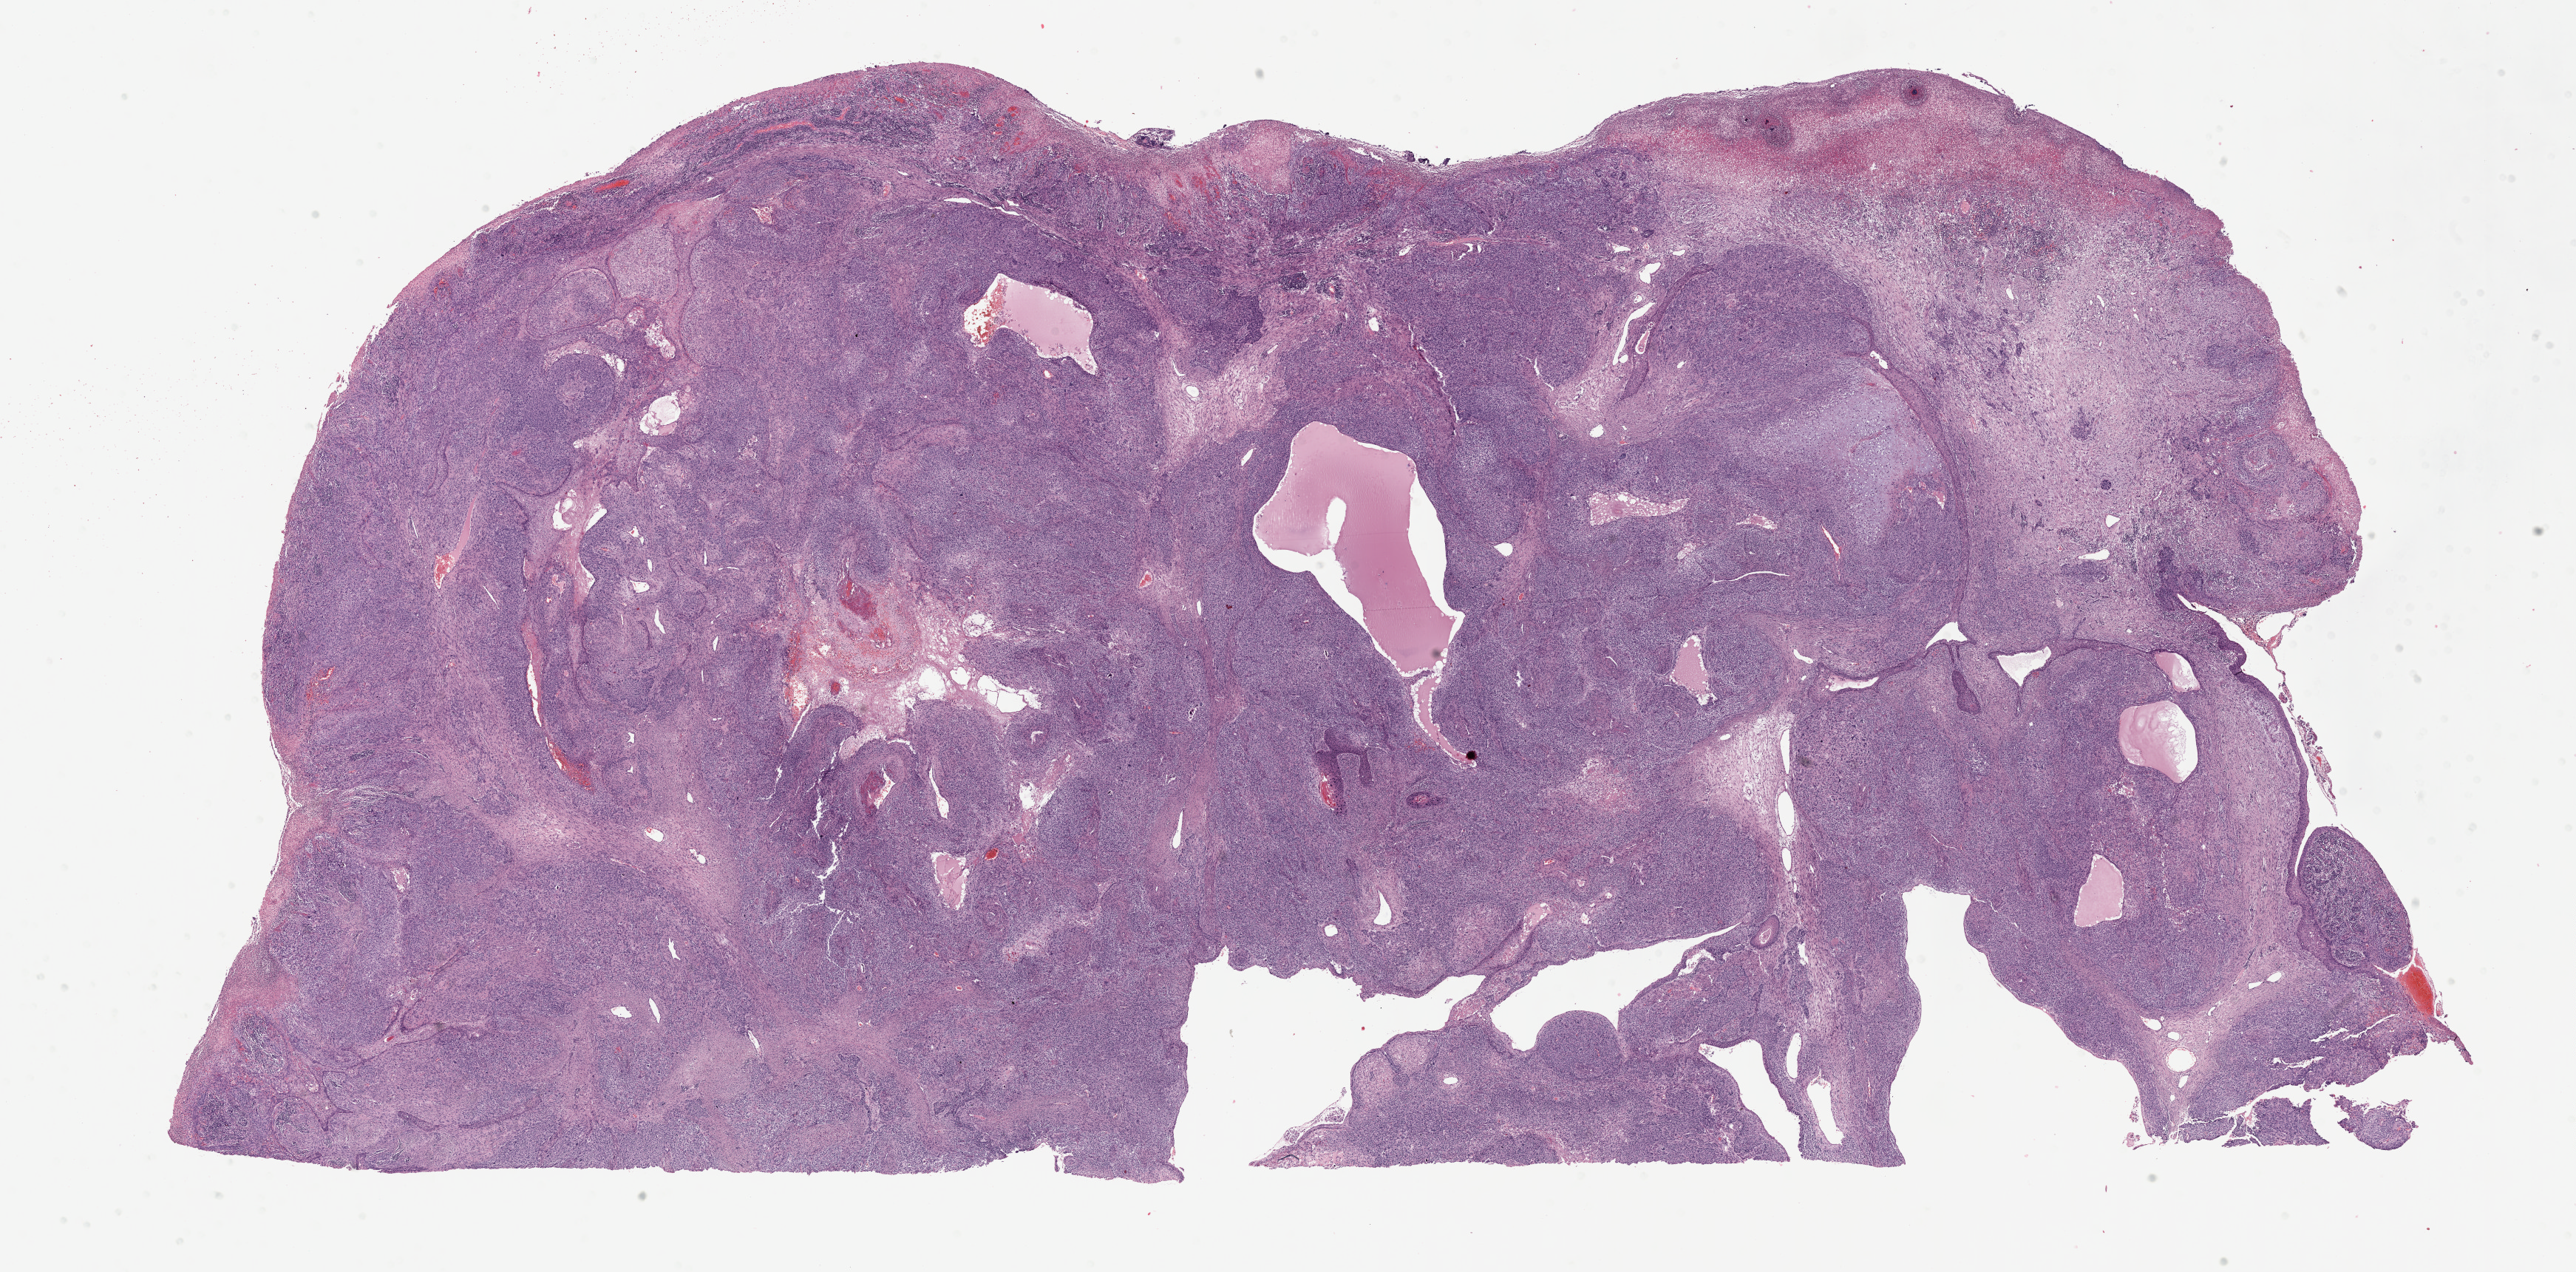
Digitized Hematoxylin and eosin (H&E) stained tissue section (whole slide) — shown as a low-resolution overview of the whole scanned area (about 28.2 x 13.9 mm); formalin-fixed paraffin-embedded (FFPE) diagnostic section; head and neck, primary tumour sample. Patient: male, age at initial diagnosis 62 years. Histologic grade: G3 (poorly differentiated).
Histologic diagnosis: Squamous cell carcinoma, large cell, nonkeratinizing, NOS (hypopharynx, NOS). AJCC pathologic stage: III. TNM: T3 N0 M0.